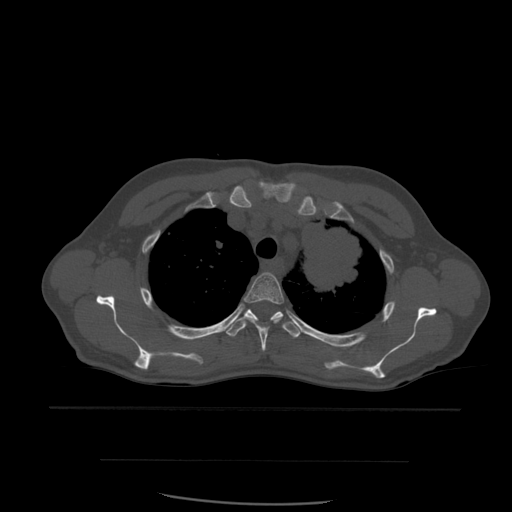
CT including the spine, one axial slice; position 436 of 574 along the scan axis; bone window (W 1800 / L 400 HU); 1.25 mm slice thickness; 512 × 512 image matrix, field of view 392 × 392 mm. Patient age 48 years. From the clinical record (not read from this slice): primary cancer: lung; vertebrae with lytic lesions (as recorded): T11.
Structures marked on this image (semi-automatic segmentation, software-assisted and operator-edited):
- T3 vertebra: bounding box (x1, y1, x2, y2) in pixels: (244, 272, 284, 352)
- T4 vertebra: (225, 309, 303, 338)